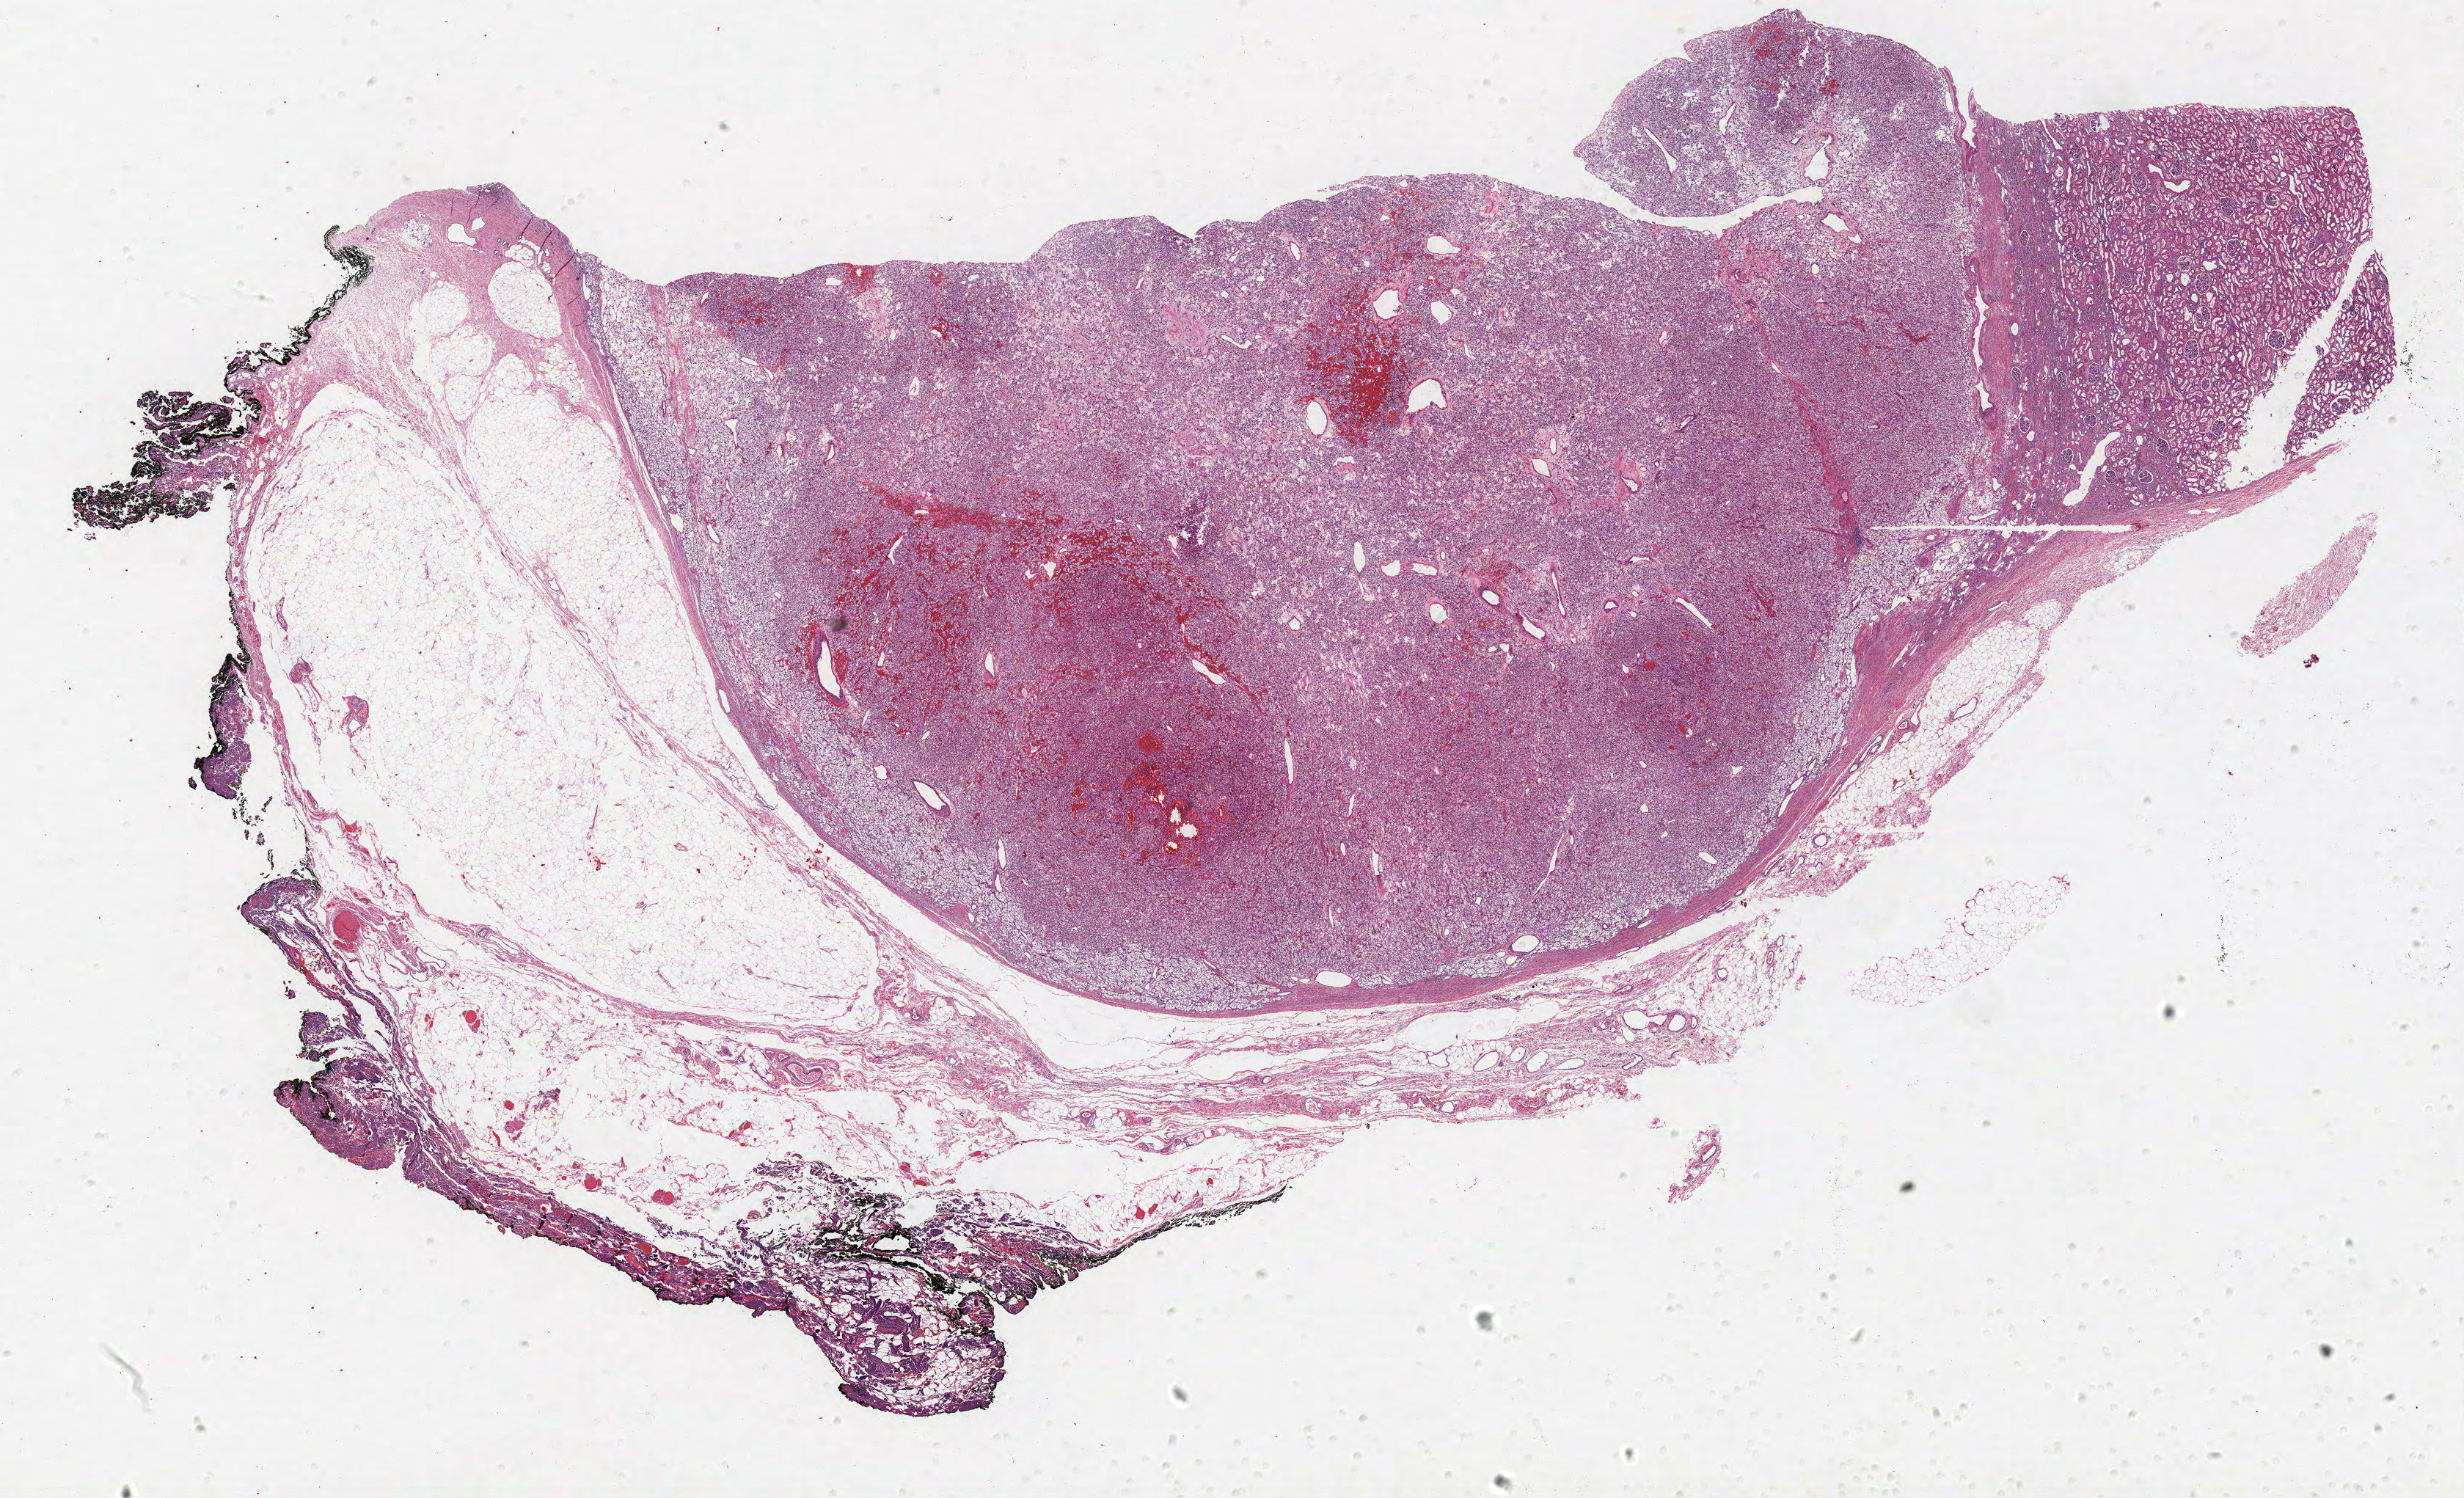
H&E-stained whole-slide image — shown as a low-resolution overview of the whole scanned area (about 26.9 x 16.3 mm, acquisition: 40x scan). Formalin-fixed paraffin-embedded (FFPE) diagnostic section. Kidney, primary tumour sample. Patient: female, age at initial diagnosis 63 years. Histologic grade: G2 (moderately differentiated).
Laterality: right. AJCC pathologic stage: I. Pathologic diagnosis: Clear cell adenocarcinoma, NOS.